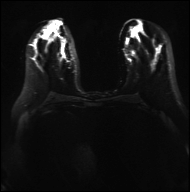
Breast MRI, one axial slice. Position 14 of 40 along the scan axis. Diffusion-weighted series; image 2 of 4 stored at this slice position (different b-values; order by instance number). 3 T. 4 mm slice thickness. 190 × 192 image matrix, field of view 317 × 320 mm. Female patient.
Structures marked on this image (expert manual segmentation):
- tumour on diffusion-weighted imaging: bounding box [x1, y1, x2, y2] px = [52, 47, 67, 53]